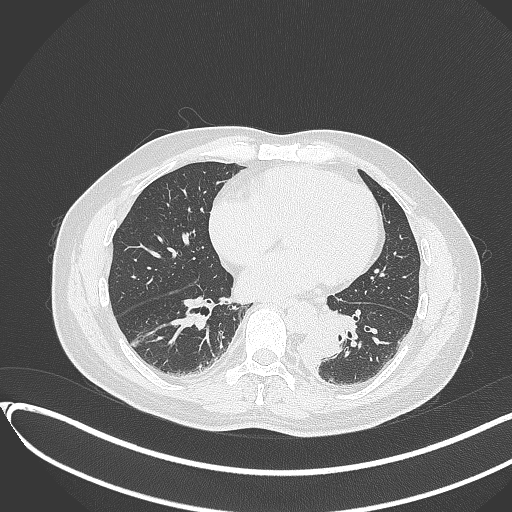
Chest CT, one axial slice. Position 132 of 417 along the scan axis. Reconstruction kernel B70f. Lung window (W 1500 / L -600 HU). 1 mm slice thickness. 512 × 512 image matrix, field of view 400 × 400 mm. Male patient, age 54 years. From the clinical record (not read from this slice): clinical TNM (as recorded): T3 N0 M0.
Annotated regions visible in this slice (rectangle marked by the reading radiologist):
- lung tumour (recorded histology: squamous cell carcinoma): box from (x=298, y=319) to (x=348, y=368) px